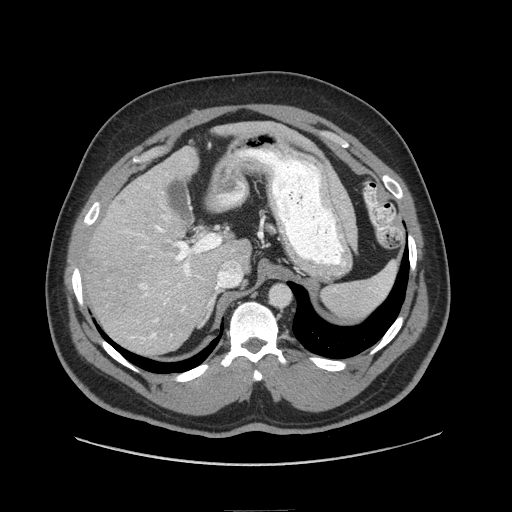
Contrast-enhanced abdominal CT (liver protocol), one axial slice; reconstruction kernel STANDARD; soft-tissue window (W 400 / L 40 HU); 2.5 mm slice thickness; 512 × 512 image matrix. From the clinical record (not read from this slice): diagnosis: hepatocellular carcinoma (patient treated with transarterial chemoembolisation; whether this scan precedes or follows treatment is not stated here); TNM stage (as recorded): Stage-II; Child-Pugh class: A.
Outlined on this slice (semi-automatically segmented with operator editing):
- liver parenchyma outside the tumour (the mass and vessels are separate outlines, so this box may not span the whole liver): bounding box <84,146,250,354> (left, top, right, bottom; pixels)
- mass: <155,235,178,260>
- liver vessels: <131,186,240,339>